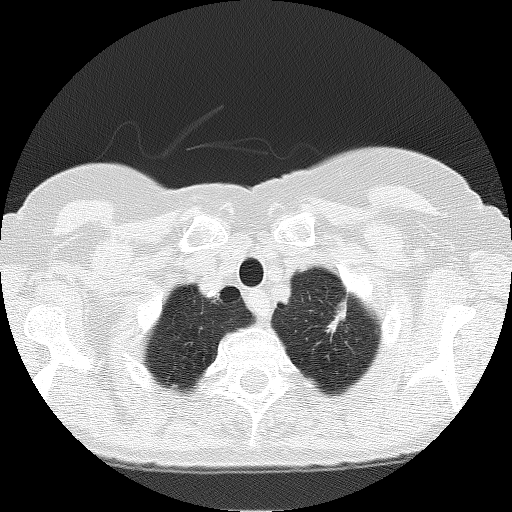
Low-dose screening chest CT, one axial slice. Reconstruction kernel FC51. 120 kVp. Lung window (W 1500 / L -600 HU). 2 mm slice thickness. 512 × 512 image matrix, field of view 303 × 303 mm.
Structures marked on this image (expert manual segmentation):
- lesion 3 (nodule, upper lobe of left lung): bounding box [x1, y1, x2, y2] px = [327, 302, 346, 333]